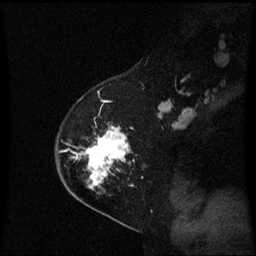
Breast MRI (dynamic contrast-enhanced), one sagittal slice. Position 41 of 60 along the scan axis. Dynamic contrast-enhanced series, image 2 of 3 at this slice position (ordered by acquisition). 1.5 T. TE 4.2 ms, TR 8.4 ms. 2 mm slice thickness. 256 × 256 image matrix. Female patient, age 54 years. From the clinical record (not read from this slice): setting: breast cancer imaged before/during neoadjuvant chemotherapy; receptor status: HER2-positive.
Structures marked on this image (semi-automatic segmentation, software-assisted and operator-edited):
- analysis volume of interest (the breast-tissue region the enhancement analysis was run in; not a lesion): bounding box (x1, y1, x2, y2) in pixels: (59, 128, 135, 199)
- tumour enhancement mask (voxels above the 70 % enhancement threshold inside the analysis volume of interest): (79, 128, 129, 189)